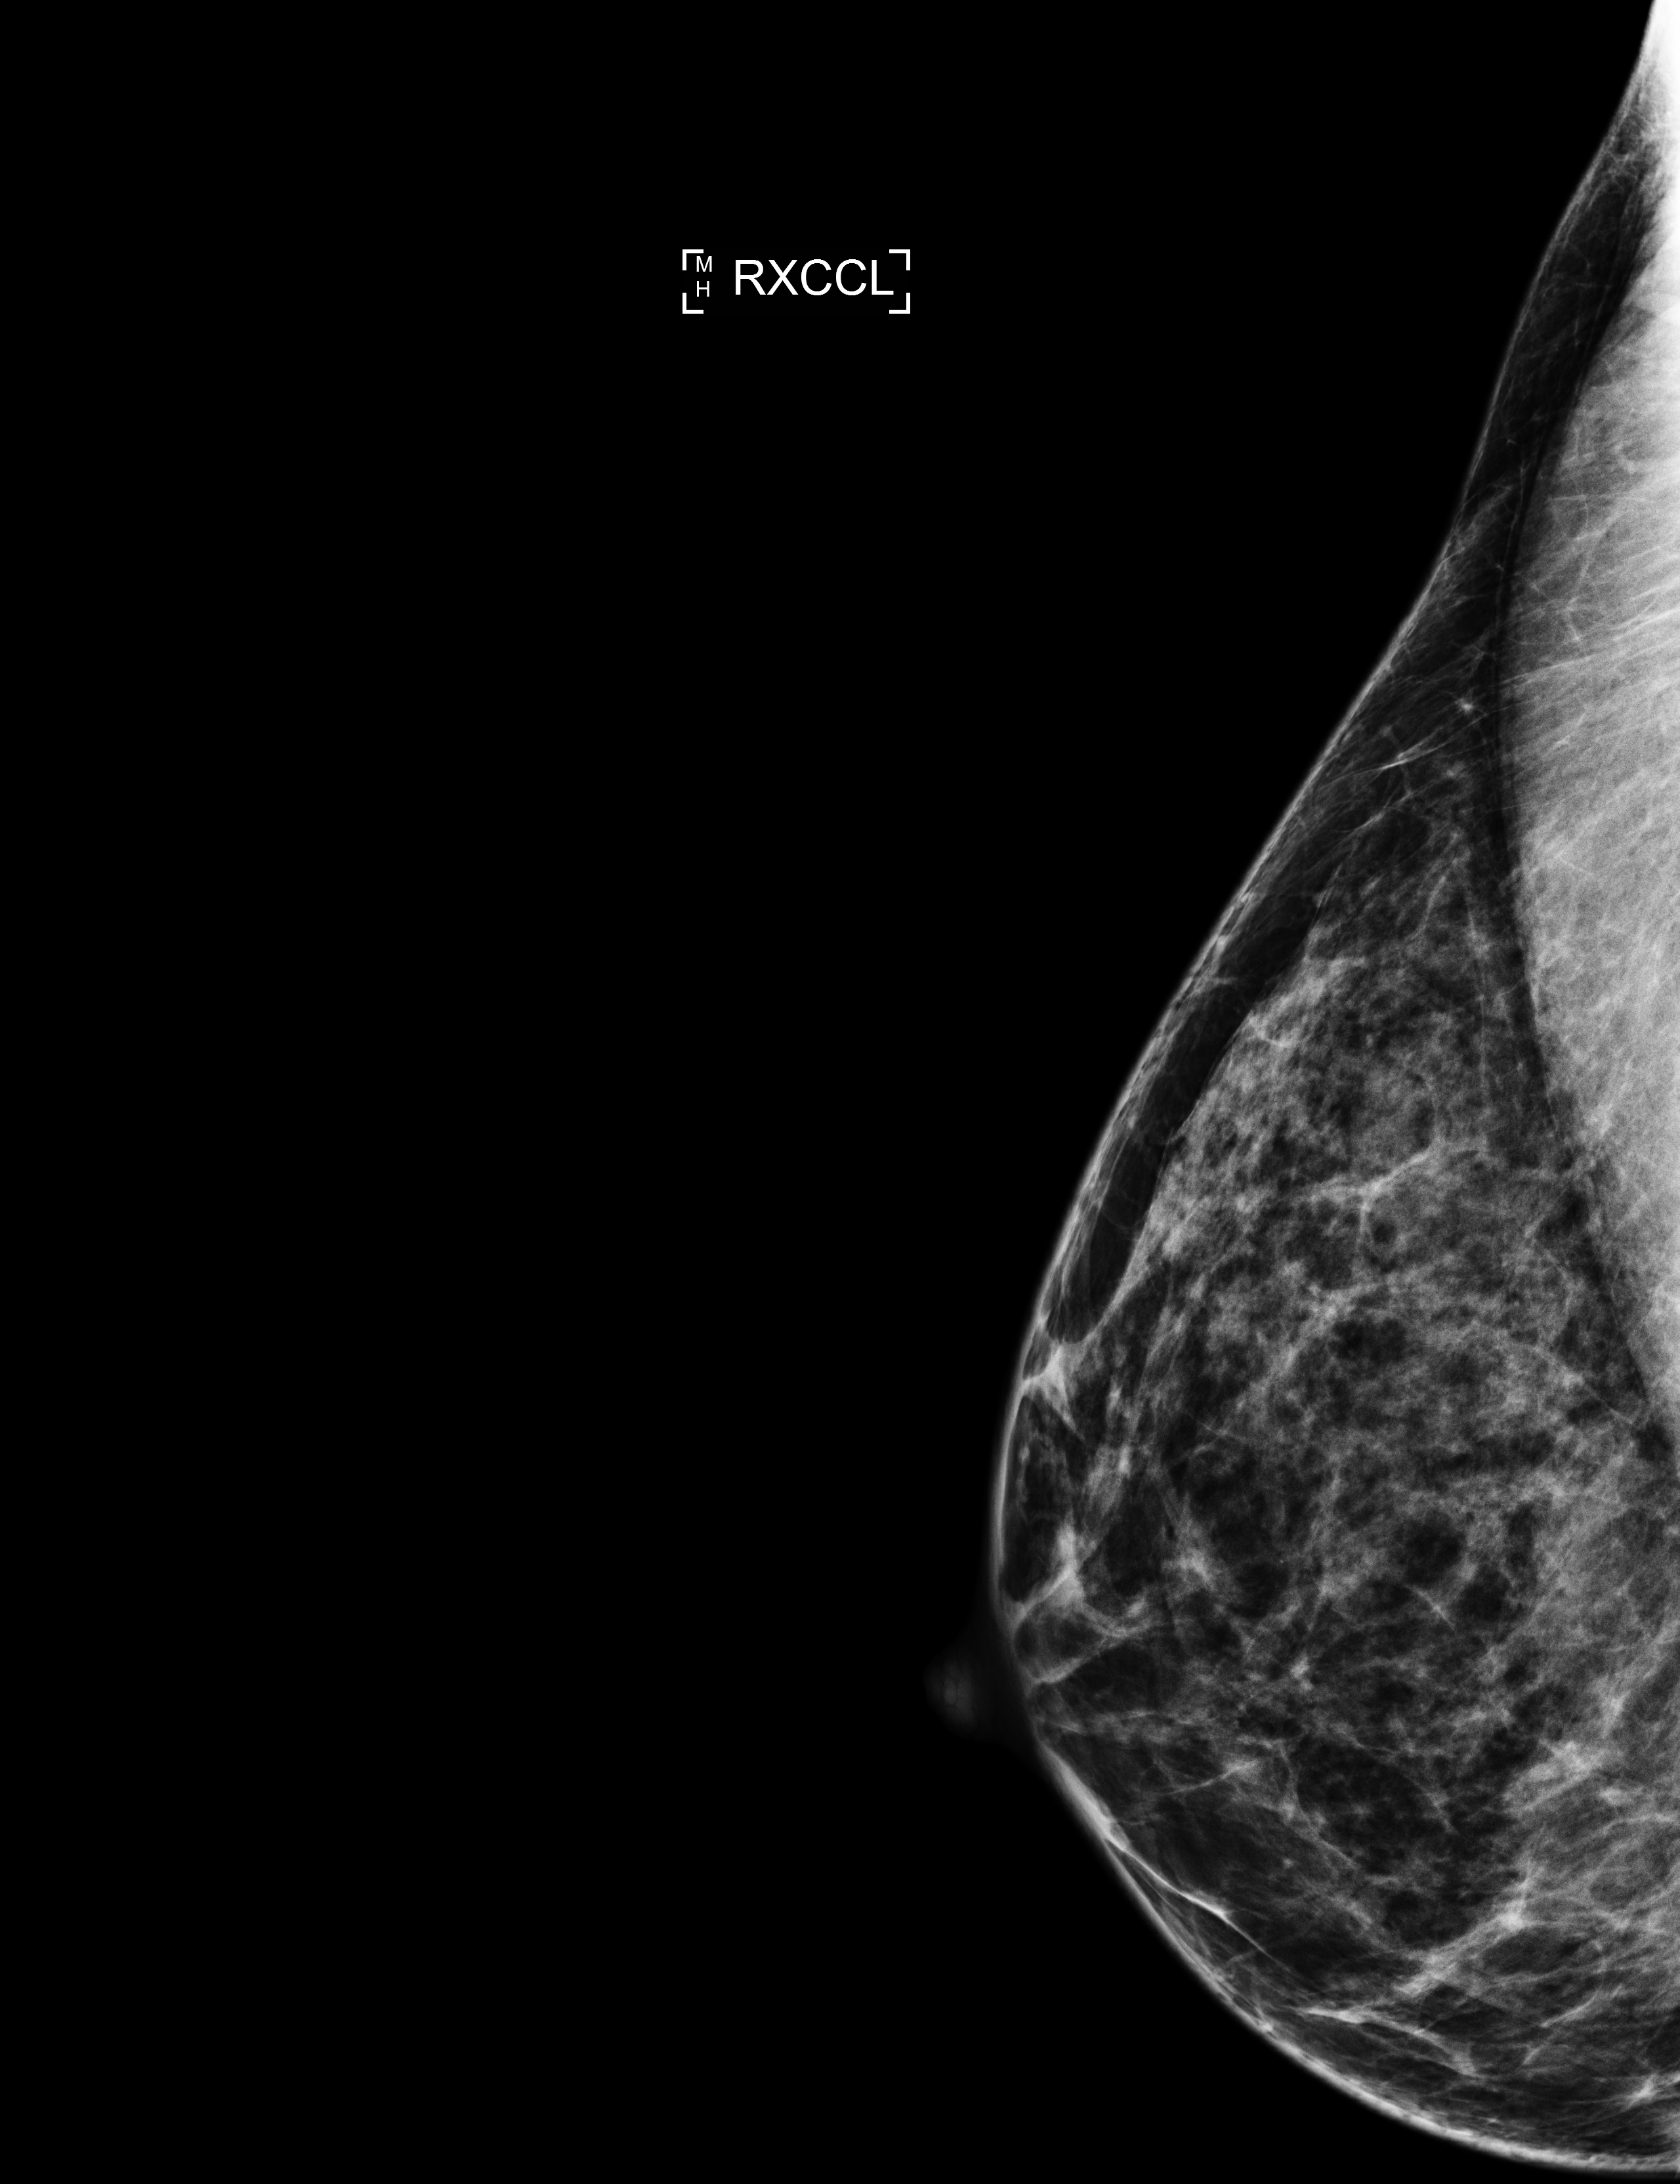
Annual screening mammography examination. Patient: female, 42 years.
Image type: full-field digital mammogram. Breast: right. Projection: exaggerated CC view (lateral).